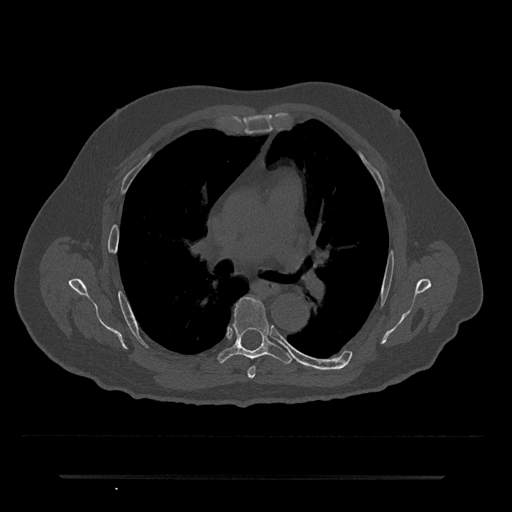
CT including the spine, one axial slice; slice 444 of 797 in the series (ordered by position); reconstruction kernel Br40s/3; 120 kVp; bone window (W 1800 / L 400 HU); 0.5 mm slice thickness; 512 × 512 image matrix, field of view 437 × 437 mm. Male patient, age 69 years. Case-level facts recorded for this patient, not image findings: primary cancer: prostate.
Annotated regions visible in this slice (semi-automatic segmentation, software-assisted and operator-edited):
- T5 vertebra: bounding box (x1, y1, x2, y2) in pixels: (247, 366, 256, 379)
- T6 vertebra: (216, 297, 293, 364)